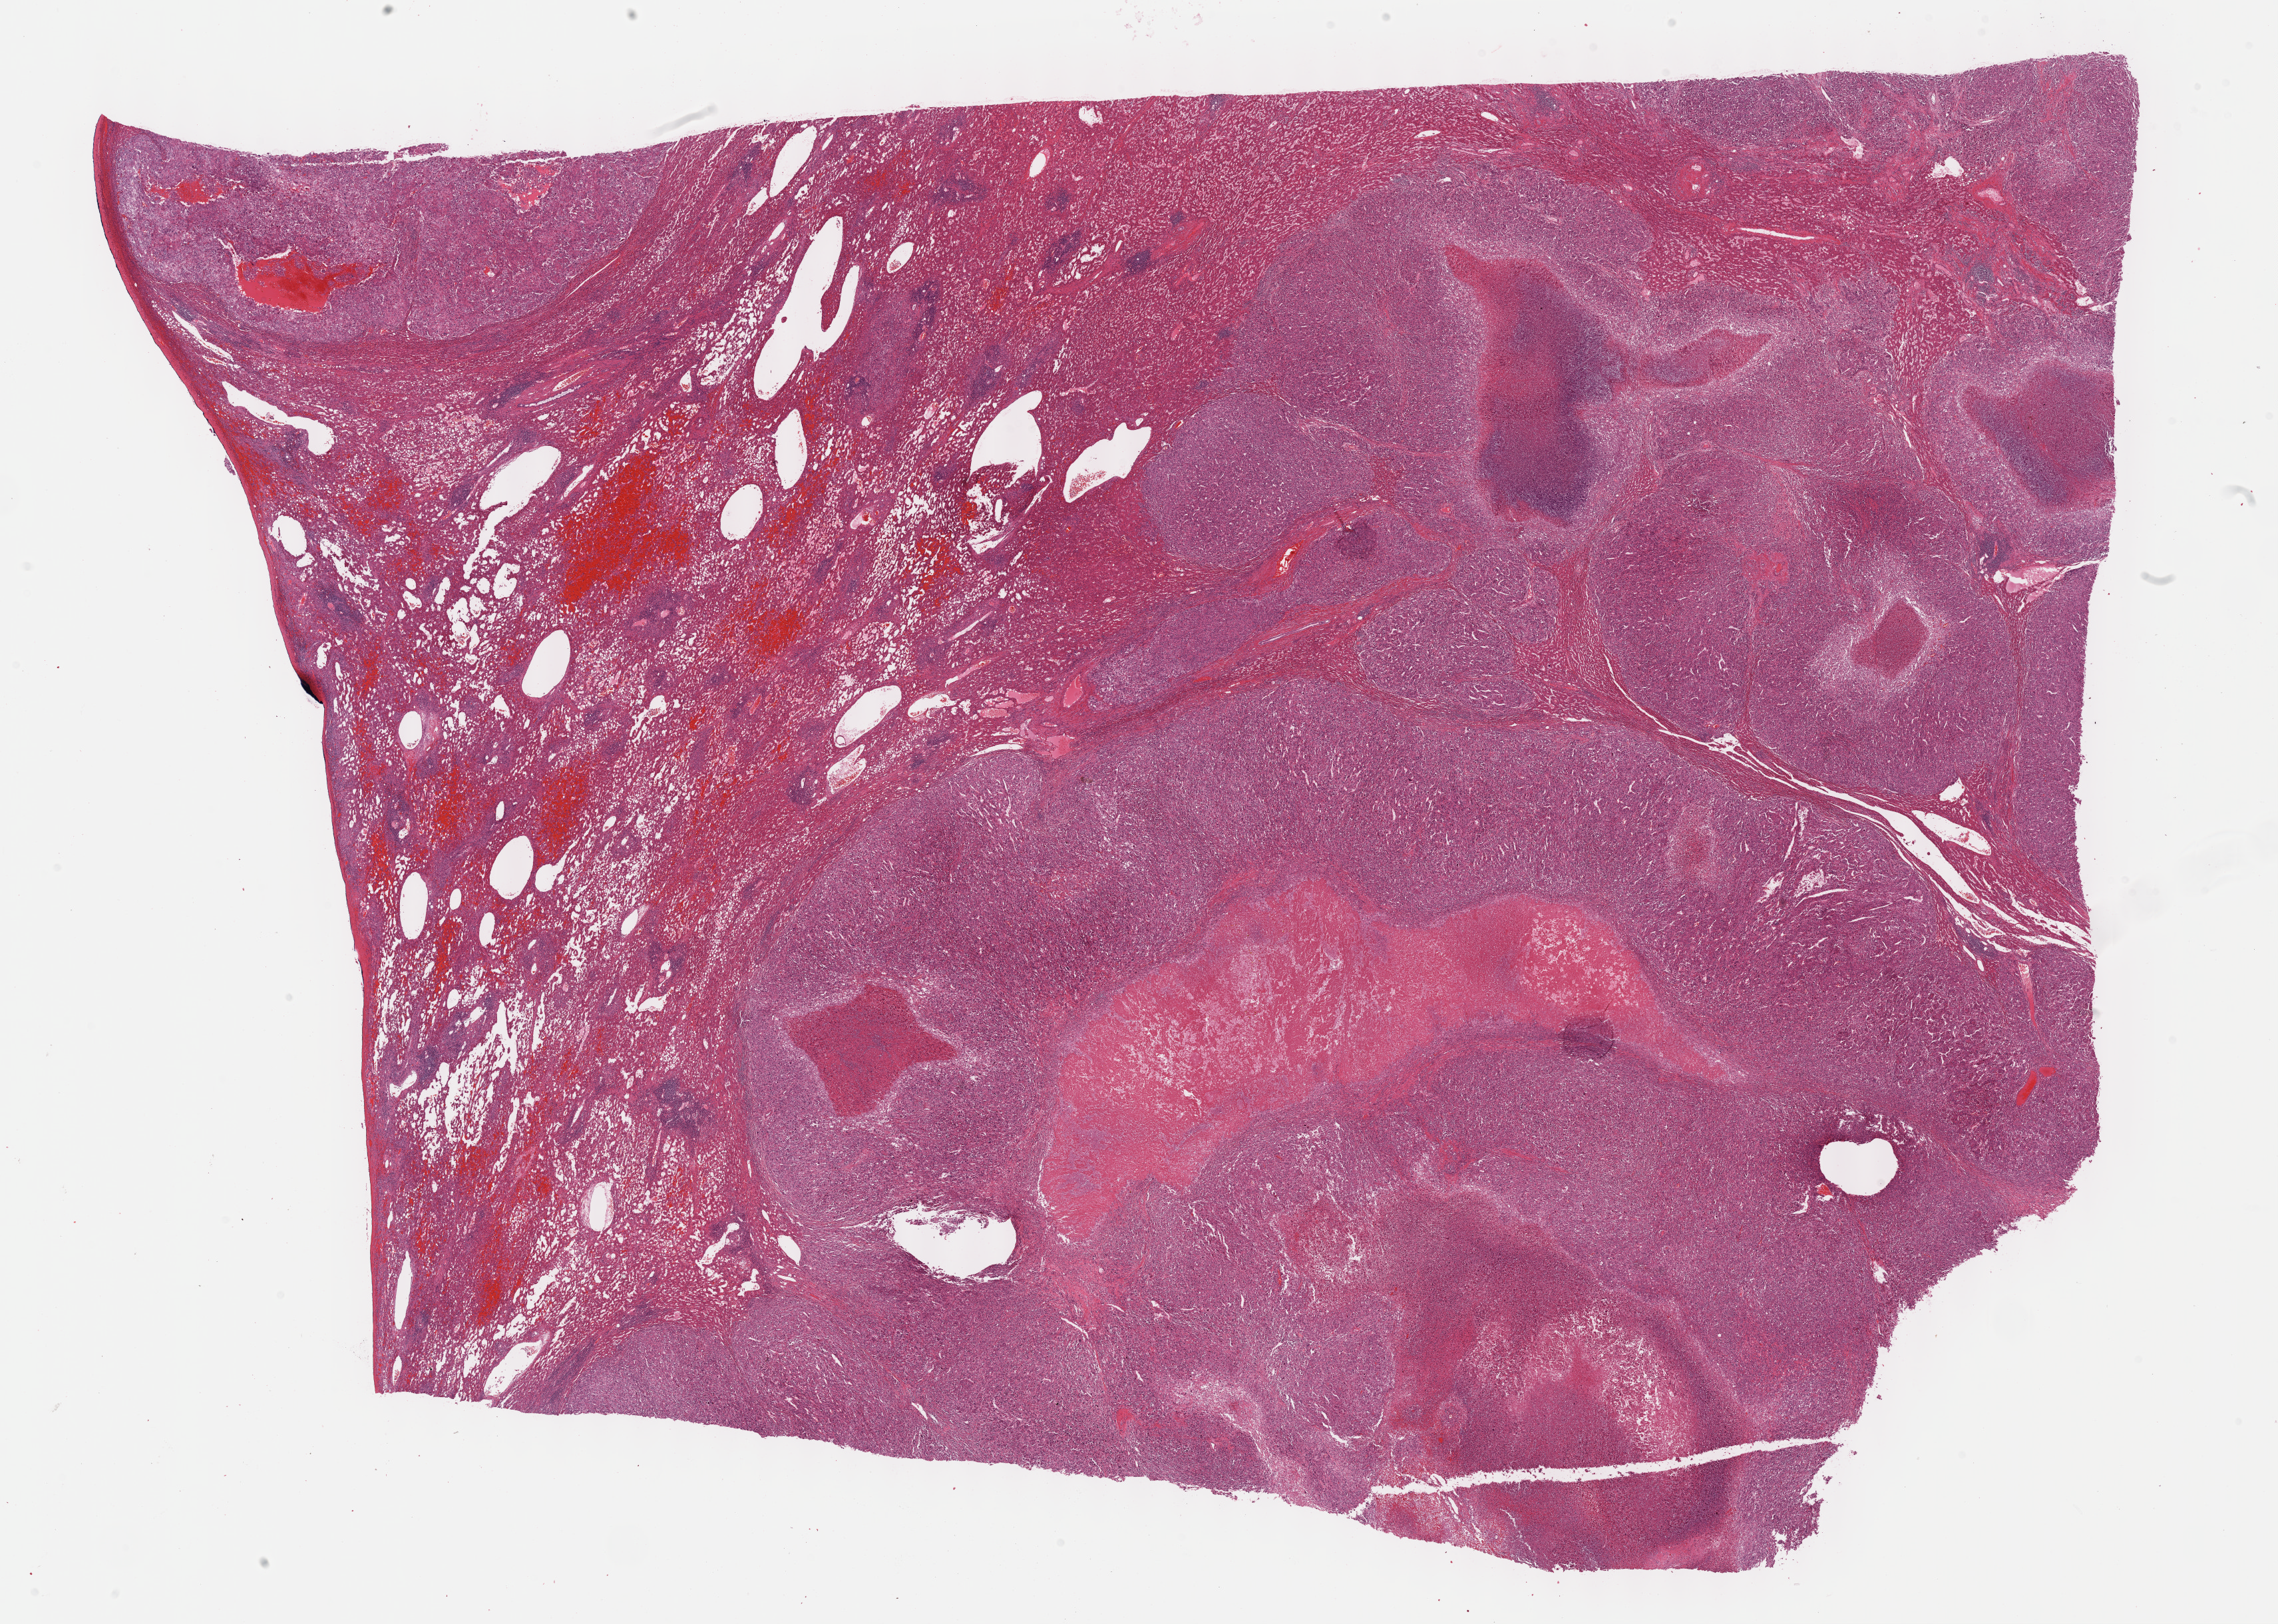
Digitized Hematoxylin and eosin (H&E) stained tissue section (whole slide) — low-resolution overview of the scanned area, about 27.7 x 19.7 mm, formalin-fixed paraffin-embedded (FFPE) diagnostic section, primary tumour sample from the liver. Male, age 68 years at initial diagnosis.
Diagnosis: Hepatocellular carcinoma, NOS.